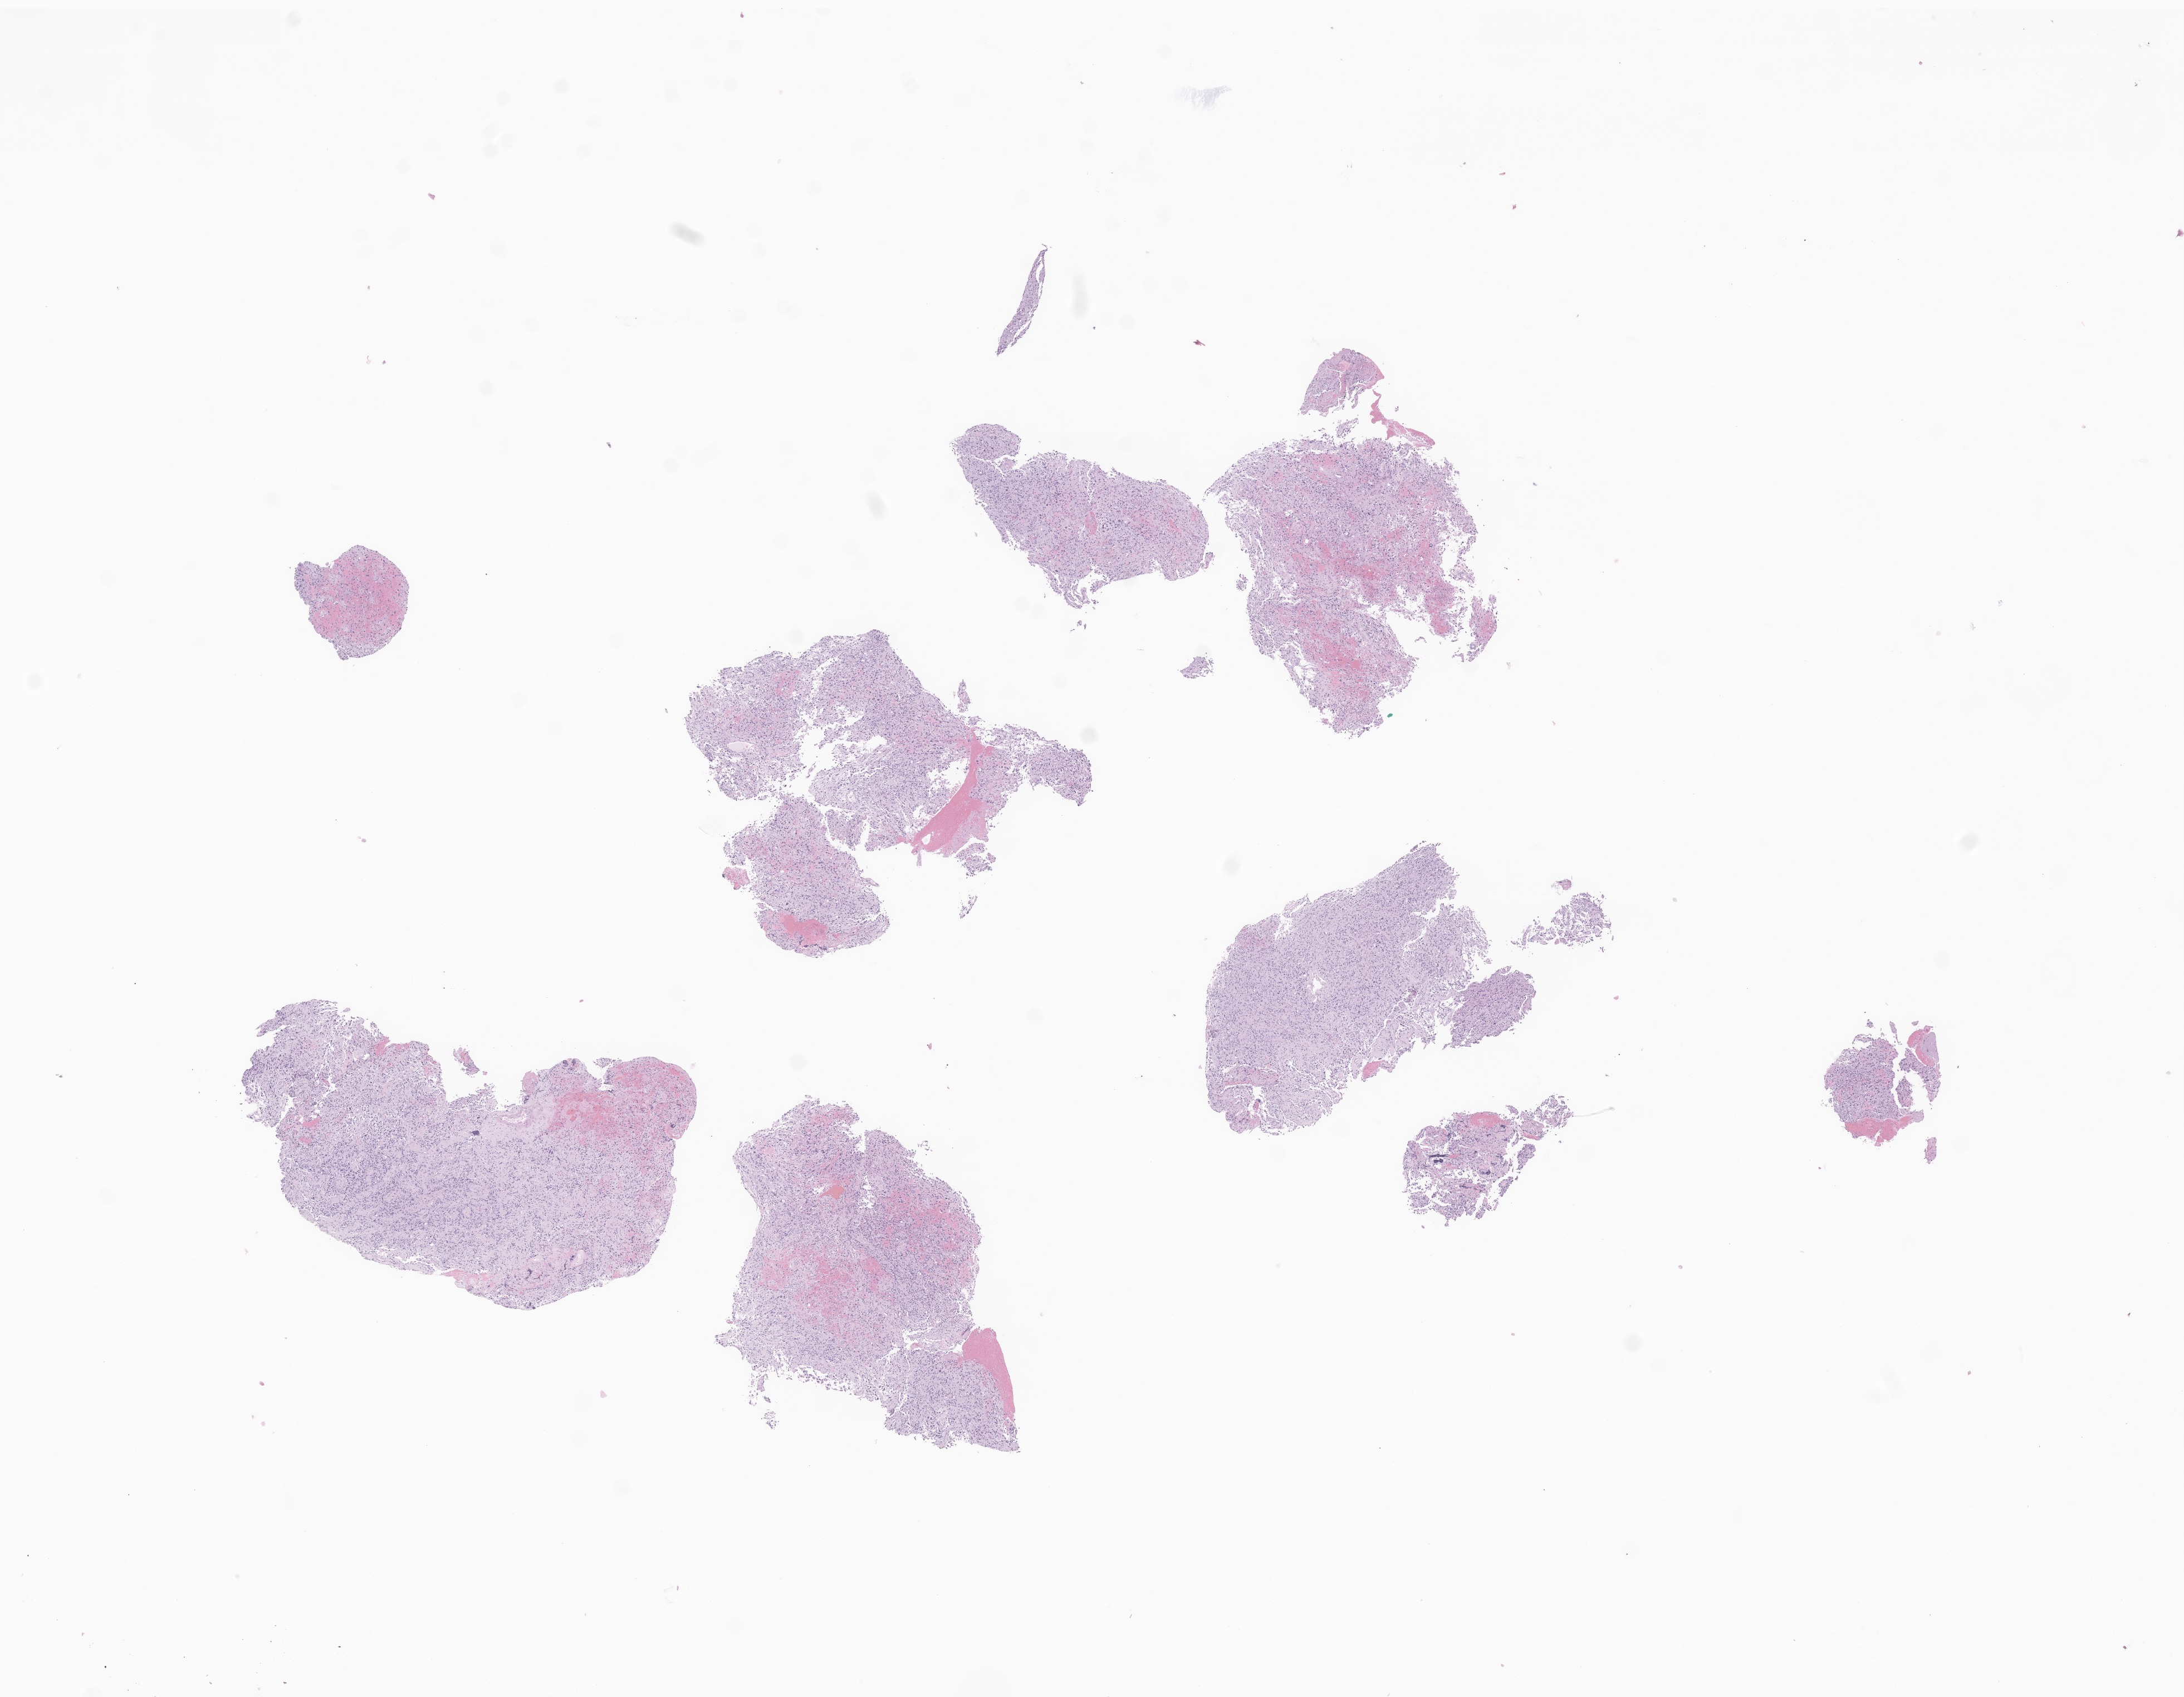
Whole-slide image, hematoxylin and eosin (H&E) stain of tumor tissue from the brain — whole scanned area (about 16.5 x 12.9 mm) shown as a low-resolution overview, formalin-fixed, paraffin-embedded (FFPE) tissue. Patient female; age 216 months (18 years).
Diagnosis (ICD-O-3 morphology term): Glioma, malignant.